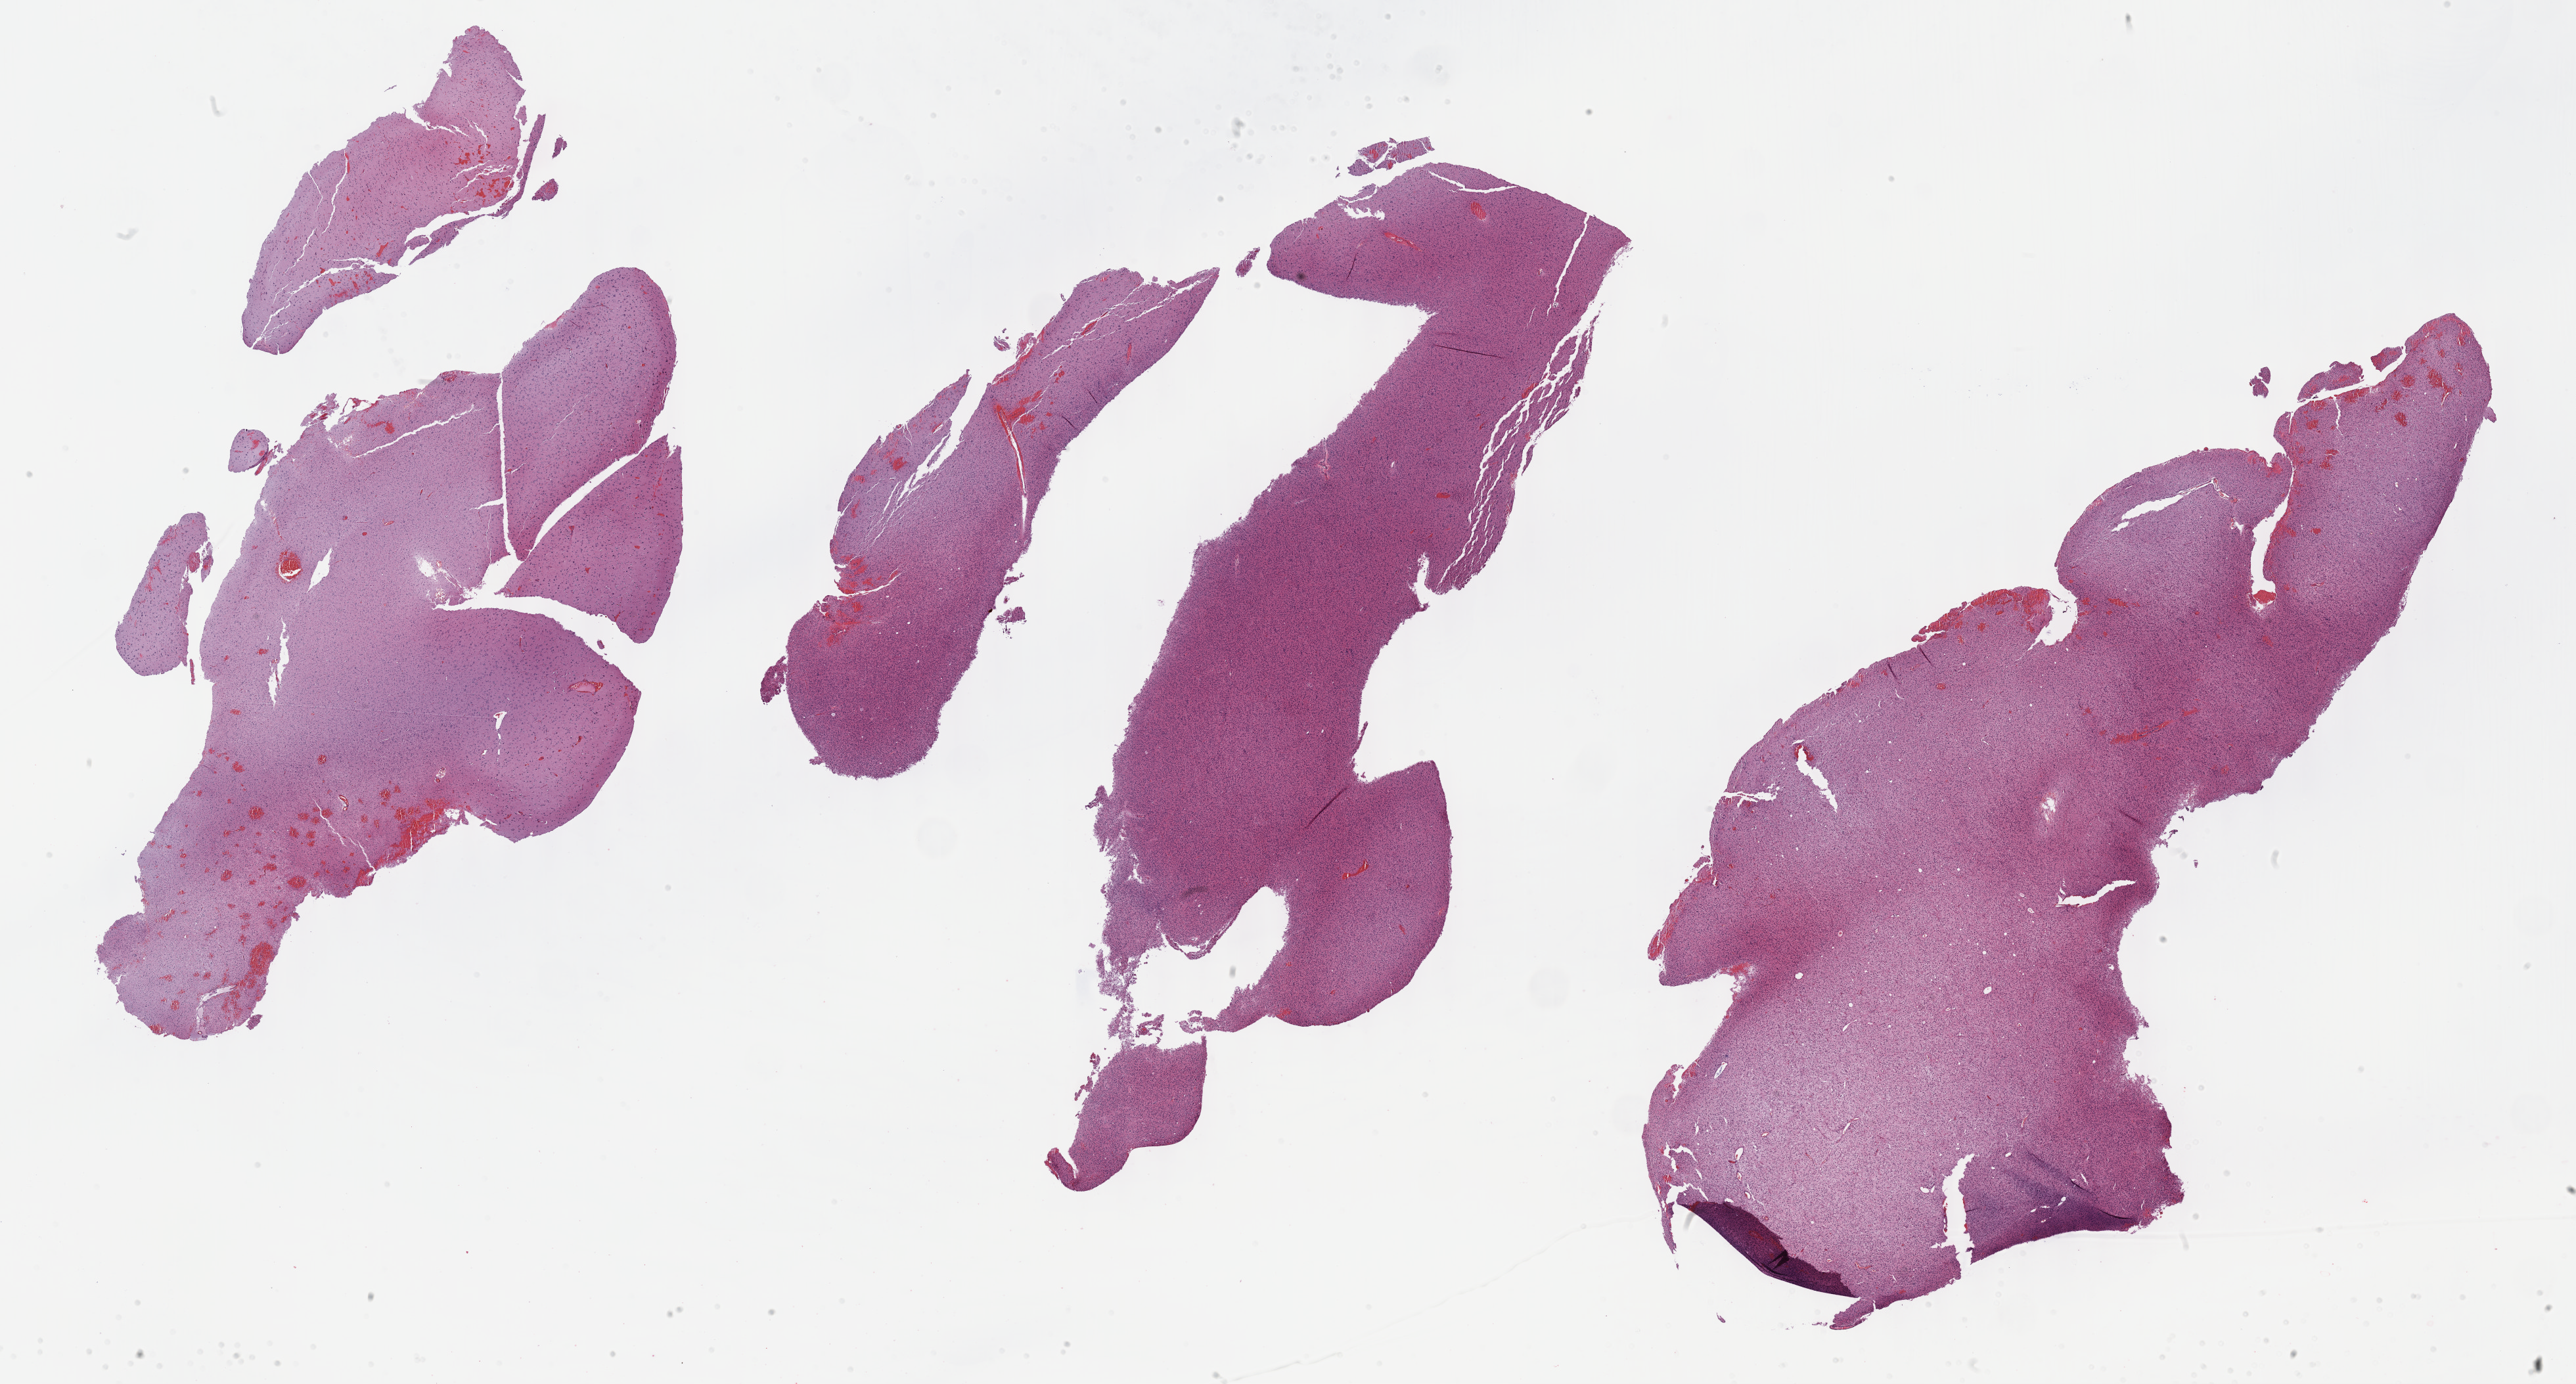
Digitized H&E-stained tissue section (whole slide) — shown as a low-resolution overview of the whole scanned area (about 31.7 x 17.0 mm), formalin-fixed paraffin-embedded (FFPE) diagnostic section, sample: primary tumour, brain. Patient: male, age at initial diagnosis 25 years. Histologic grade: G2 (moderately differentiated).
Pathologic diagnosis: Oligodendroglioma, NOS (cerebrum).